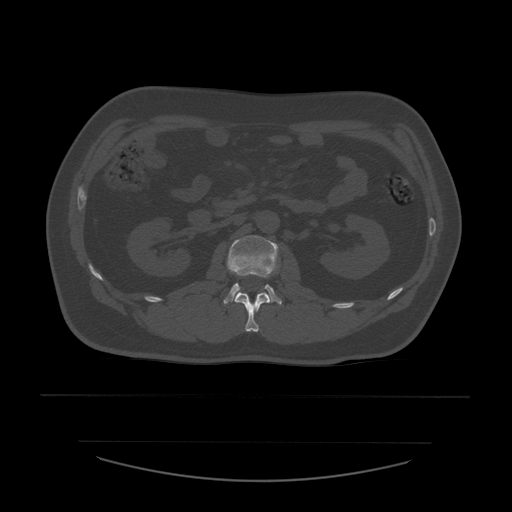
CT including the spine, one axial slice. Slice 213 of 532 in the series (ordered by position). 120 kVp. Bone window (W 1800 / L 400 HU). 1.25 mm slice thickness. 512 × 512 image matrix. Patient age 44 years. From the clinical record (not read from this slice): primary cancer: soft tissue sarcoma.
Outlined on this slice (semi-automatically segmented with operator editing):
- L1 vertebra: bounding box [x1, y1, x2, y2] px = [235, 292, 272, 332]
- L2 vertebra: [224, 236, 282, 305]